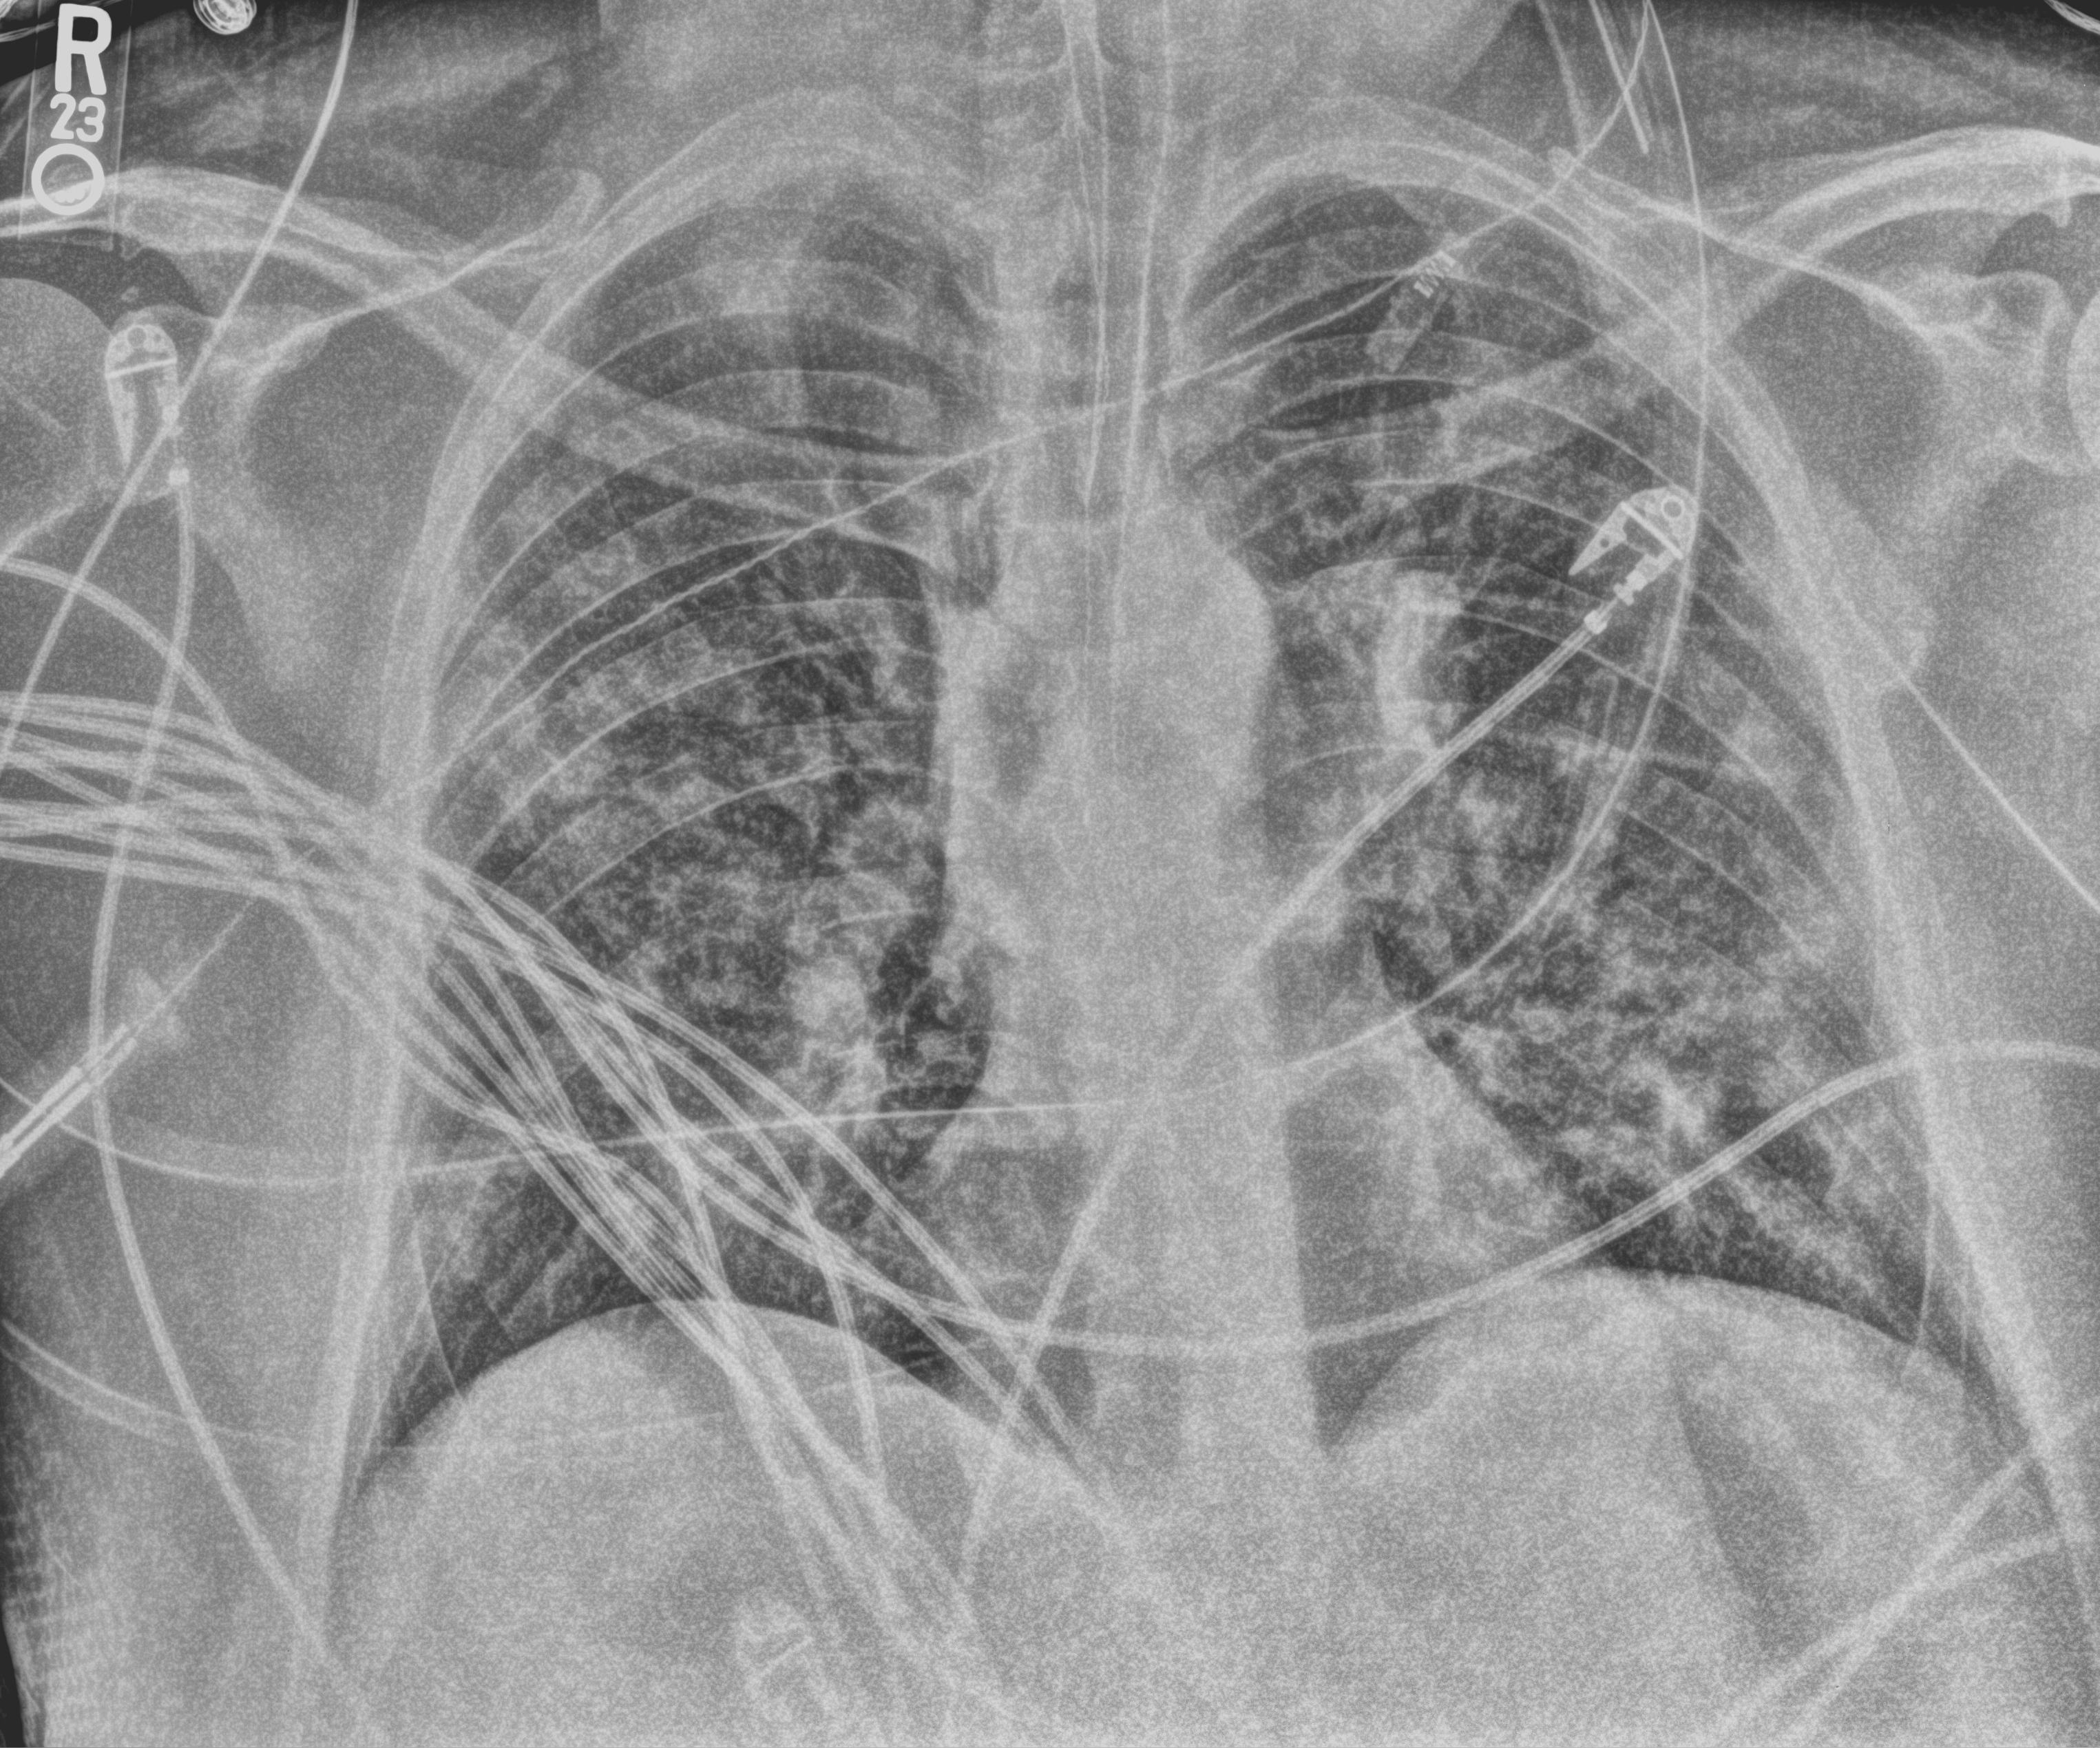
Portable chest radiograph, anteroposterior (AP) projection. Patient hospitalised with COVID-19, aged 18–59 years.
Hospital-stay facts (about this admission, not read from this image; timing relative to this image not recorded): diabetes (admission record): no; mechanically ventilated during this hospital stay: yes.